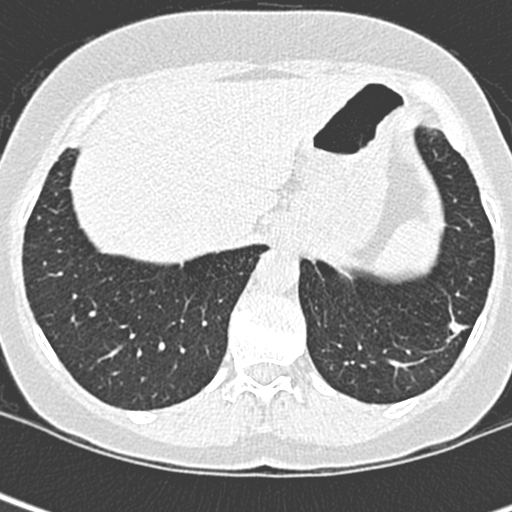
Low-dose screening chest CT, one axial slice. Slice 57 of 252 in the series (ordered by position). Lung window (W 1500 / L -600 HU). 1.3 mm slice thickness. 512 × 512 image matrix, field of view 271 × 271 mm.
Structures marked on this image (outlined manually by an expert reader):
- lesion 1 (tumor, lower lobe of left lung): bounding box [x1, y1, x2, y2] px = [449, 317, 464, 334]